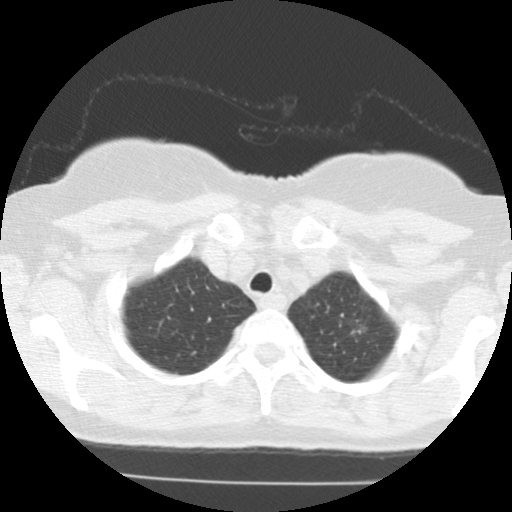
Low-dose screening chest CT, axial slice. Baseline screening round. Lung window (W 1500 / L -600 HU). 2.5 mm slice thickness. Standard (soft-tissue) reconstruction kernel (STANDARD). Female participant, aged 61 years at enrolment. Former smoker at enrolment.
Expert reader's lesion annotation, bounding box <324,304,375,354> (left, top, right, bottom; pixels). The screening reader recorded 2 non-calcified nodules or masses ≥4 mm on this exam; which of them this box marks is not recorded. Official screen result: positive, change unspecified: nodule(s) >= 4 mm or enlarging nodule(s), mass(es), or other non-specific abnormalities suspicious for lung cancer. Participant outcome: lung cancer diagnosed 79 days after this screen — adenocarcinoma, NOS, left upper lobe, stage IIIB (AJCC 6th edition), 15 mm at pathology.